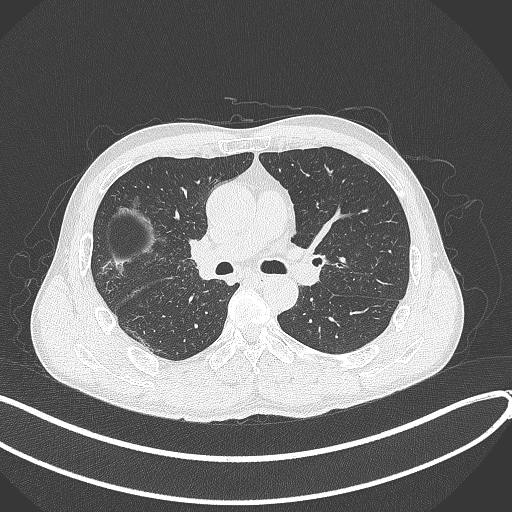
Chest CT, one axial slice. Reconstruction kernel B70f. 120 kVp. Lung window (W 1500 / L -600 HU). 1 mm slice thickness. 512 × 512 image matrix, field of view 400 × 400 mm. Male patient, age 53 years. From the clinical record (not read from this slice): clinical TNM (as recorded): T1b N0 M0.
Structures marked on this image (rectangle marked by the reading radiologist):
- lung tumour (recorded histology: squamous cell carcinoma): bounding box (x1, y1, x2, y2) in pixels: (183, 231, 221, 280)